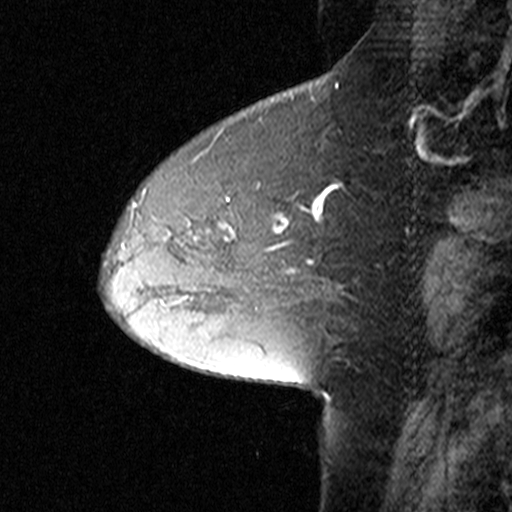
Breast MRI (dynamic contrast-enhanced), one sagittal slice; position 15 of 44 along the scan axis; dynamic contrast-enhanced study with each time point stored as its own series, time point 2 of 3 at this slice position (early post-contrast, ordered by acquisition time); 1.5 T; TE 4.5 ms, TR 11 ms; 512 × 512 image matrix. Patient: female, 50 years. Case-level facts recorded for this patient, not image findings: setting: breast cancer imaged before/during neoadjuvant chemotherapy; receptor status: HR-positive, HER2-negative.
Outlined on this slice (semi-automatic segmentation, software-assisted and operator-edited):
- analysis volume of interest (the breast-tissue region the enhancement analysis was run in; not a lesion): box from (x=126, y=162) to (x=296, y=291) px
- tumour enhancement mask (voxels above the 90 % enhancement threshold inside the analysis volume of interest): (x=132, y=198)–(x=295, y=272)